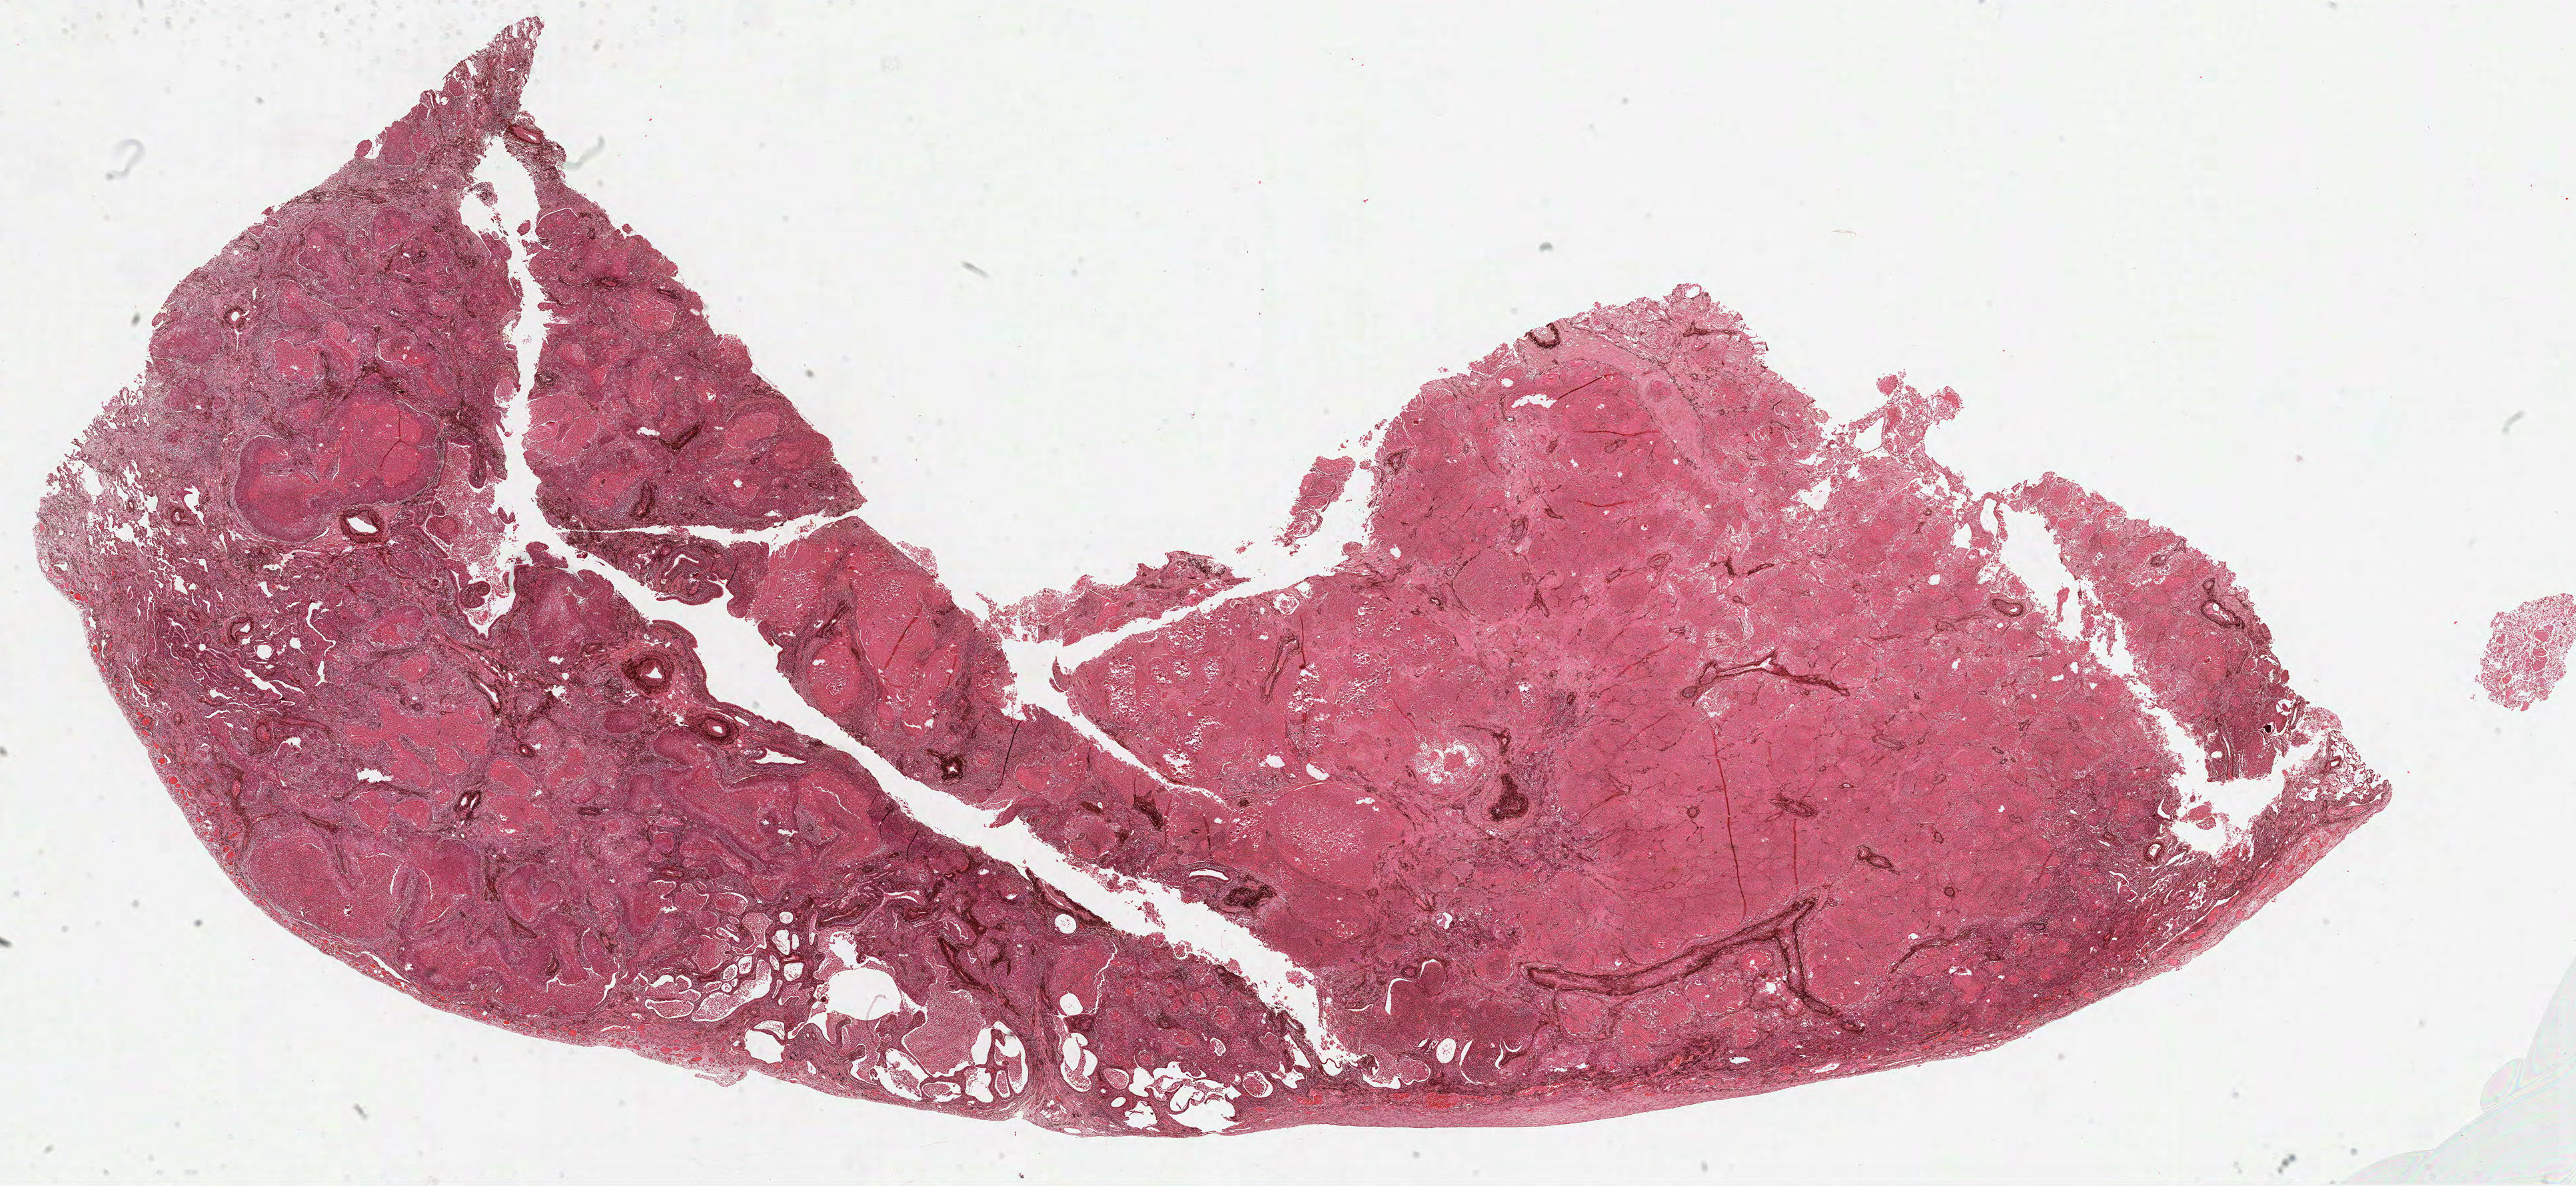
H&E-stained whole-slide image — whole scanned area (about 31.2 x 14.4 mm, acquisition: 40x scan) shown as a low-resolution overview. Formalin-fixed paraffin-embedded (FFPE) diagnostic section. Sample: primary tumour, lung. Patient: male, age at initial diagnosis 72 years.
Histologic diagnosis: Squamous cell carcinoma, NOS (lower lobe, lung). TNM: T2 NX M0. AJCC pathologic stage: IB (6th edition).